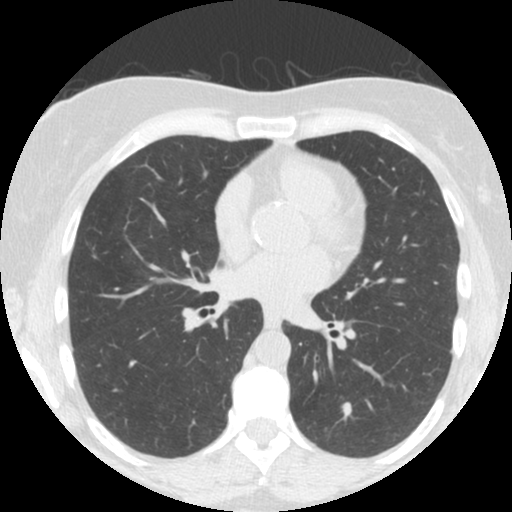
Low-dose screening chest CT, one axial slice. Position 77 of 150 along the scan axis. Reconstruction kernel STANDARD. 120 kVp. Lung window (W 1500 / L -600 HU). 2.5 mm slice thickness. 512 × 512 image matrix, field of view 300 × 300 mm.
Structures marked on this image (outlined manually by an expert reader):
- lesion 1 (tumor, lower lobe of left lung): bounding box (x1, y1, x2, y2) in pixels: (342, 402, 352, 418)